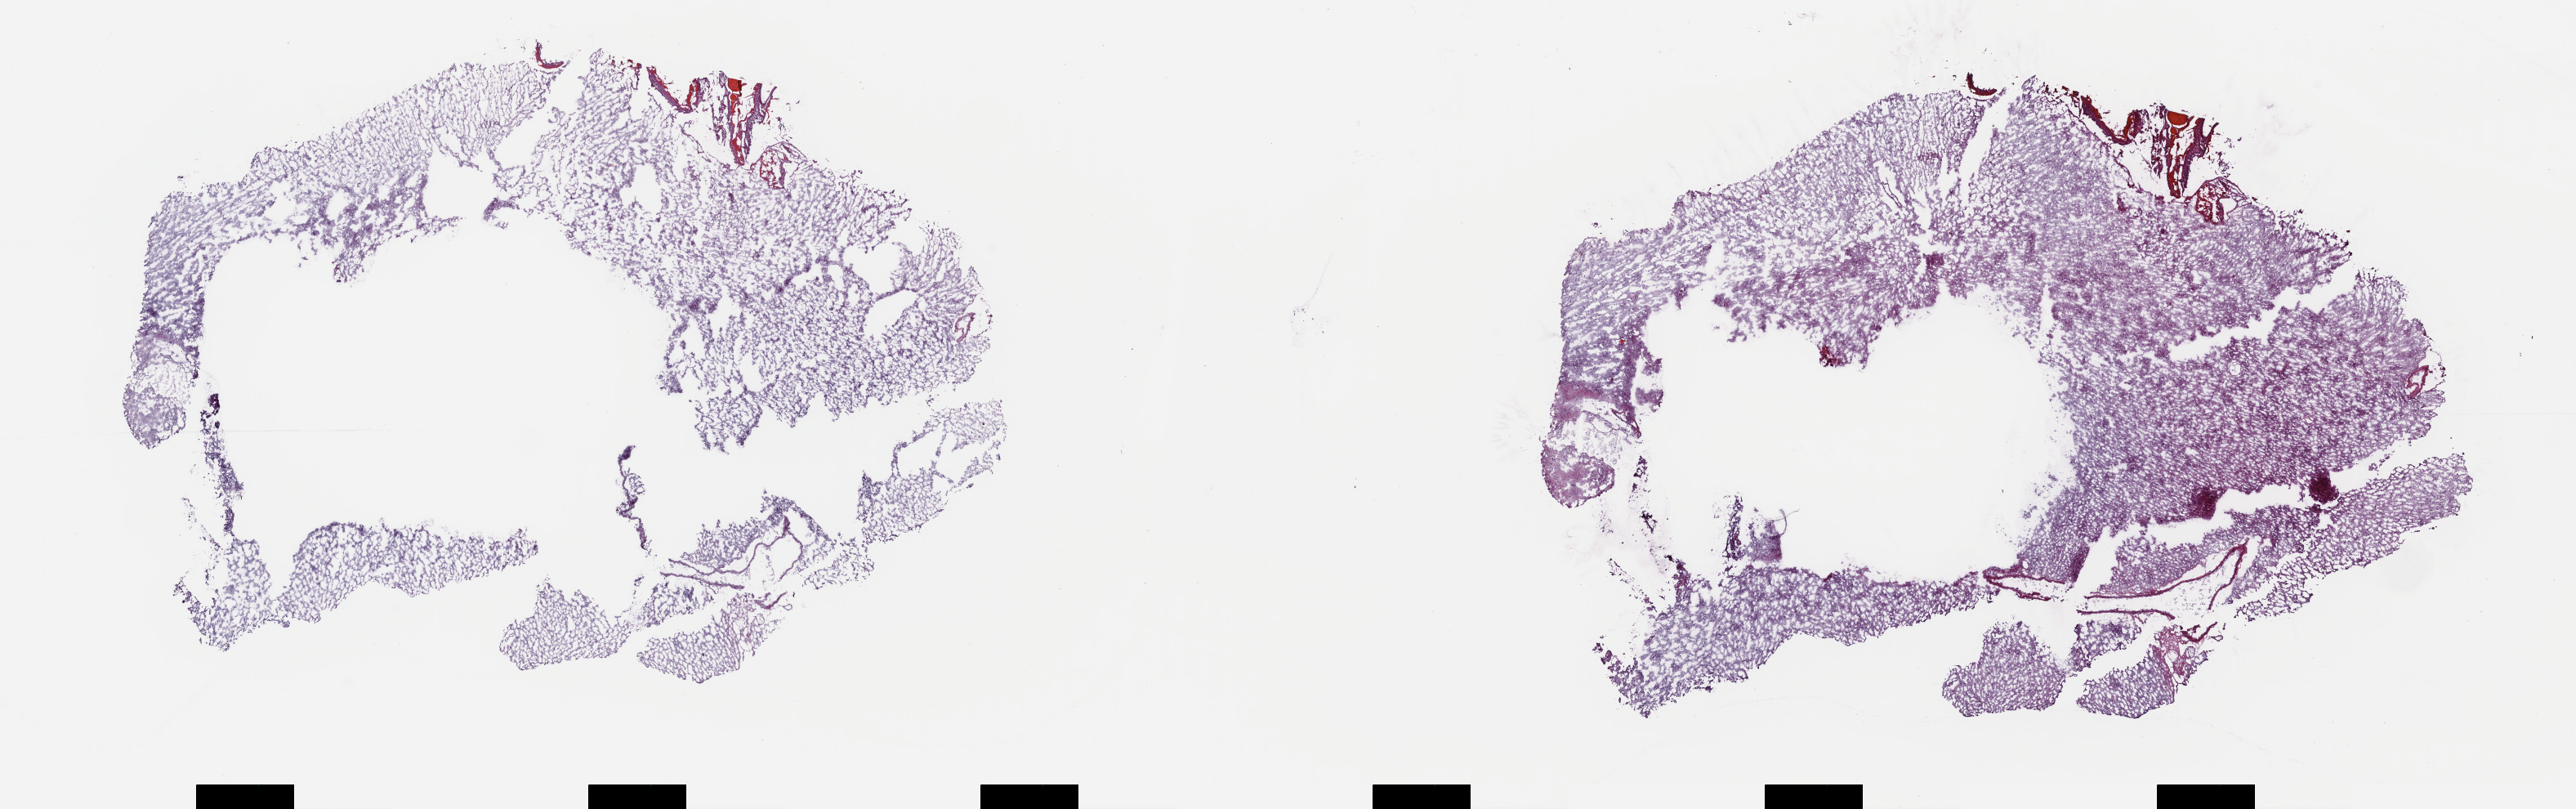
Digitized H&E tissue section (whole slide), whole scanned area (about 24.9 x 7.8 mm, acquisition: 40x scan) shown as a low-resolution overview. Frozen section from the top of the tissue portion. Sample: primary tumour, brain. Patient: female, age at initial diagnosis 33 years. Histologic grade: G2 (moderately differentiated). Slide review estimates, as recorded: tumour cells 50%, tumour nuclei 70%, normal cells 5%, stromal cells 45%, necrosis 0%. Inflammatory infiltration, as recorded: lymphocyte infiltration 0%, monocyte infiltration 0%, neutrophil infiltration 0%.
Histologic diagnosis: Oligodendroglioma, NOS (cerebrum).